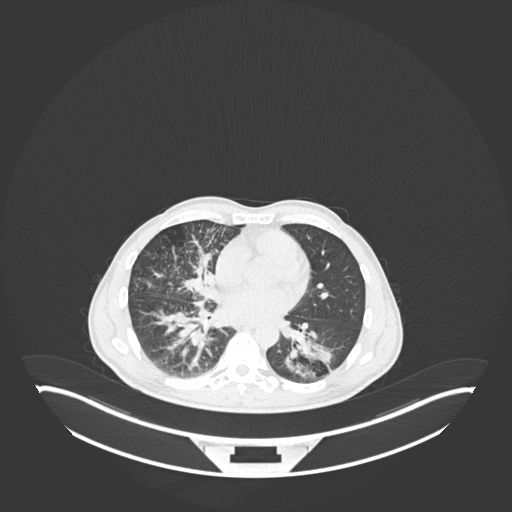
Chest CT, one axial slice; slice 106 of 237 in the series (ordered by position); reconstruction kernel B30f; lung window (W 1500 / L -600 HU); 1 mm slice thickness; 512 × 512 image matrix, field of view 500 × 500 mm. Male patient, age 49 years. Case-level facts recorded for this patient, not image findings: clinical TNM (as recorded): T2b N1 M0.
Annotated regions visible in this slice (bounding box drawn by a radiologist):
- lung tumour (recorded histology: adenocarcinoma): box from (x=282, y=328) to (x=343, y=386) px